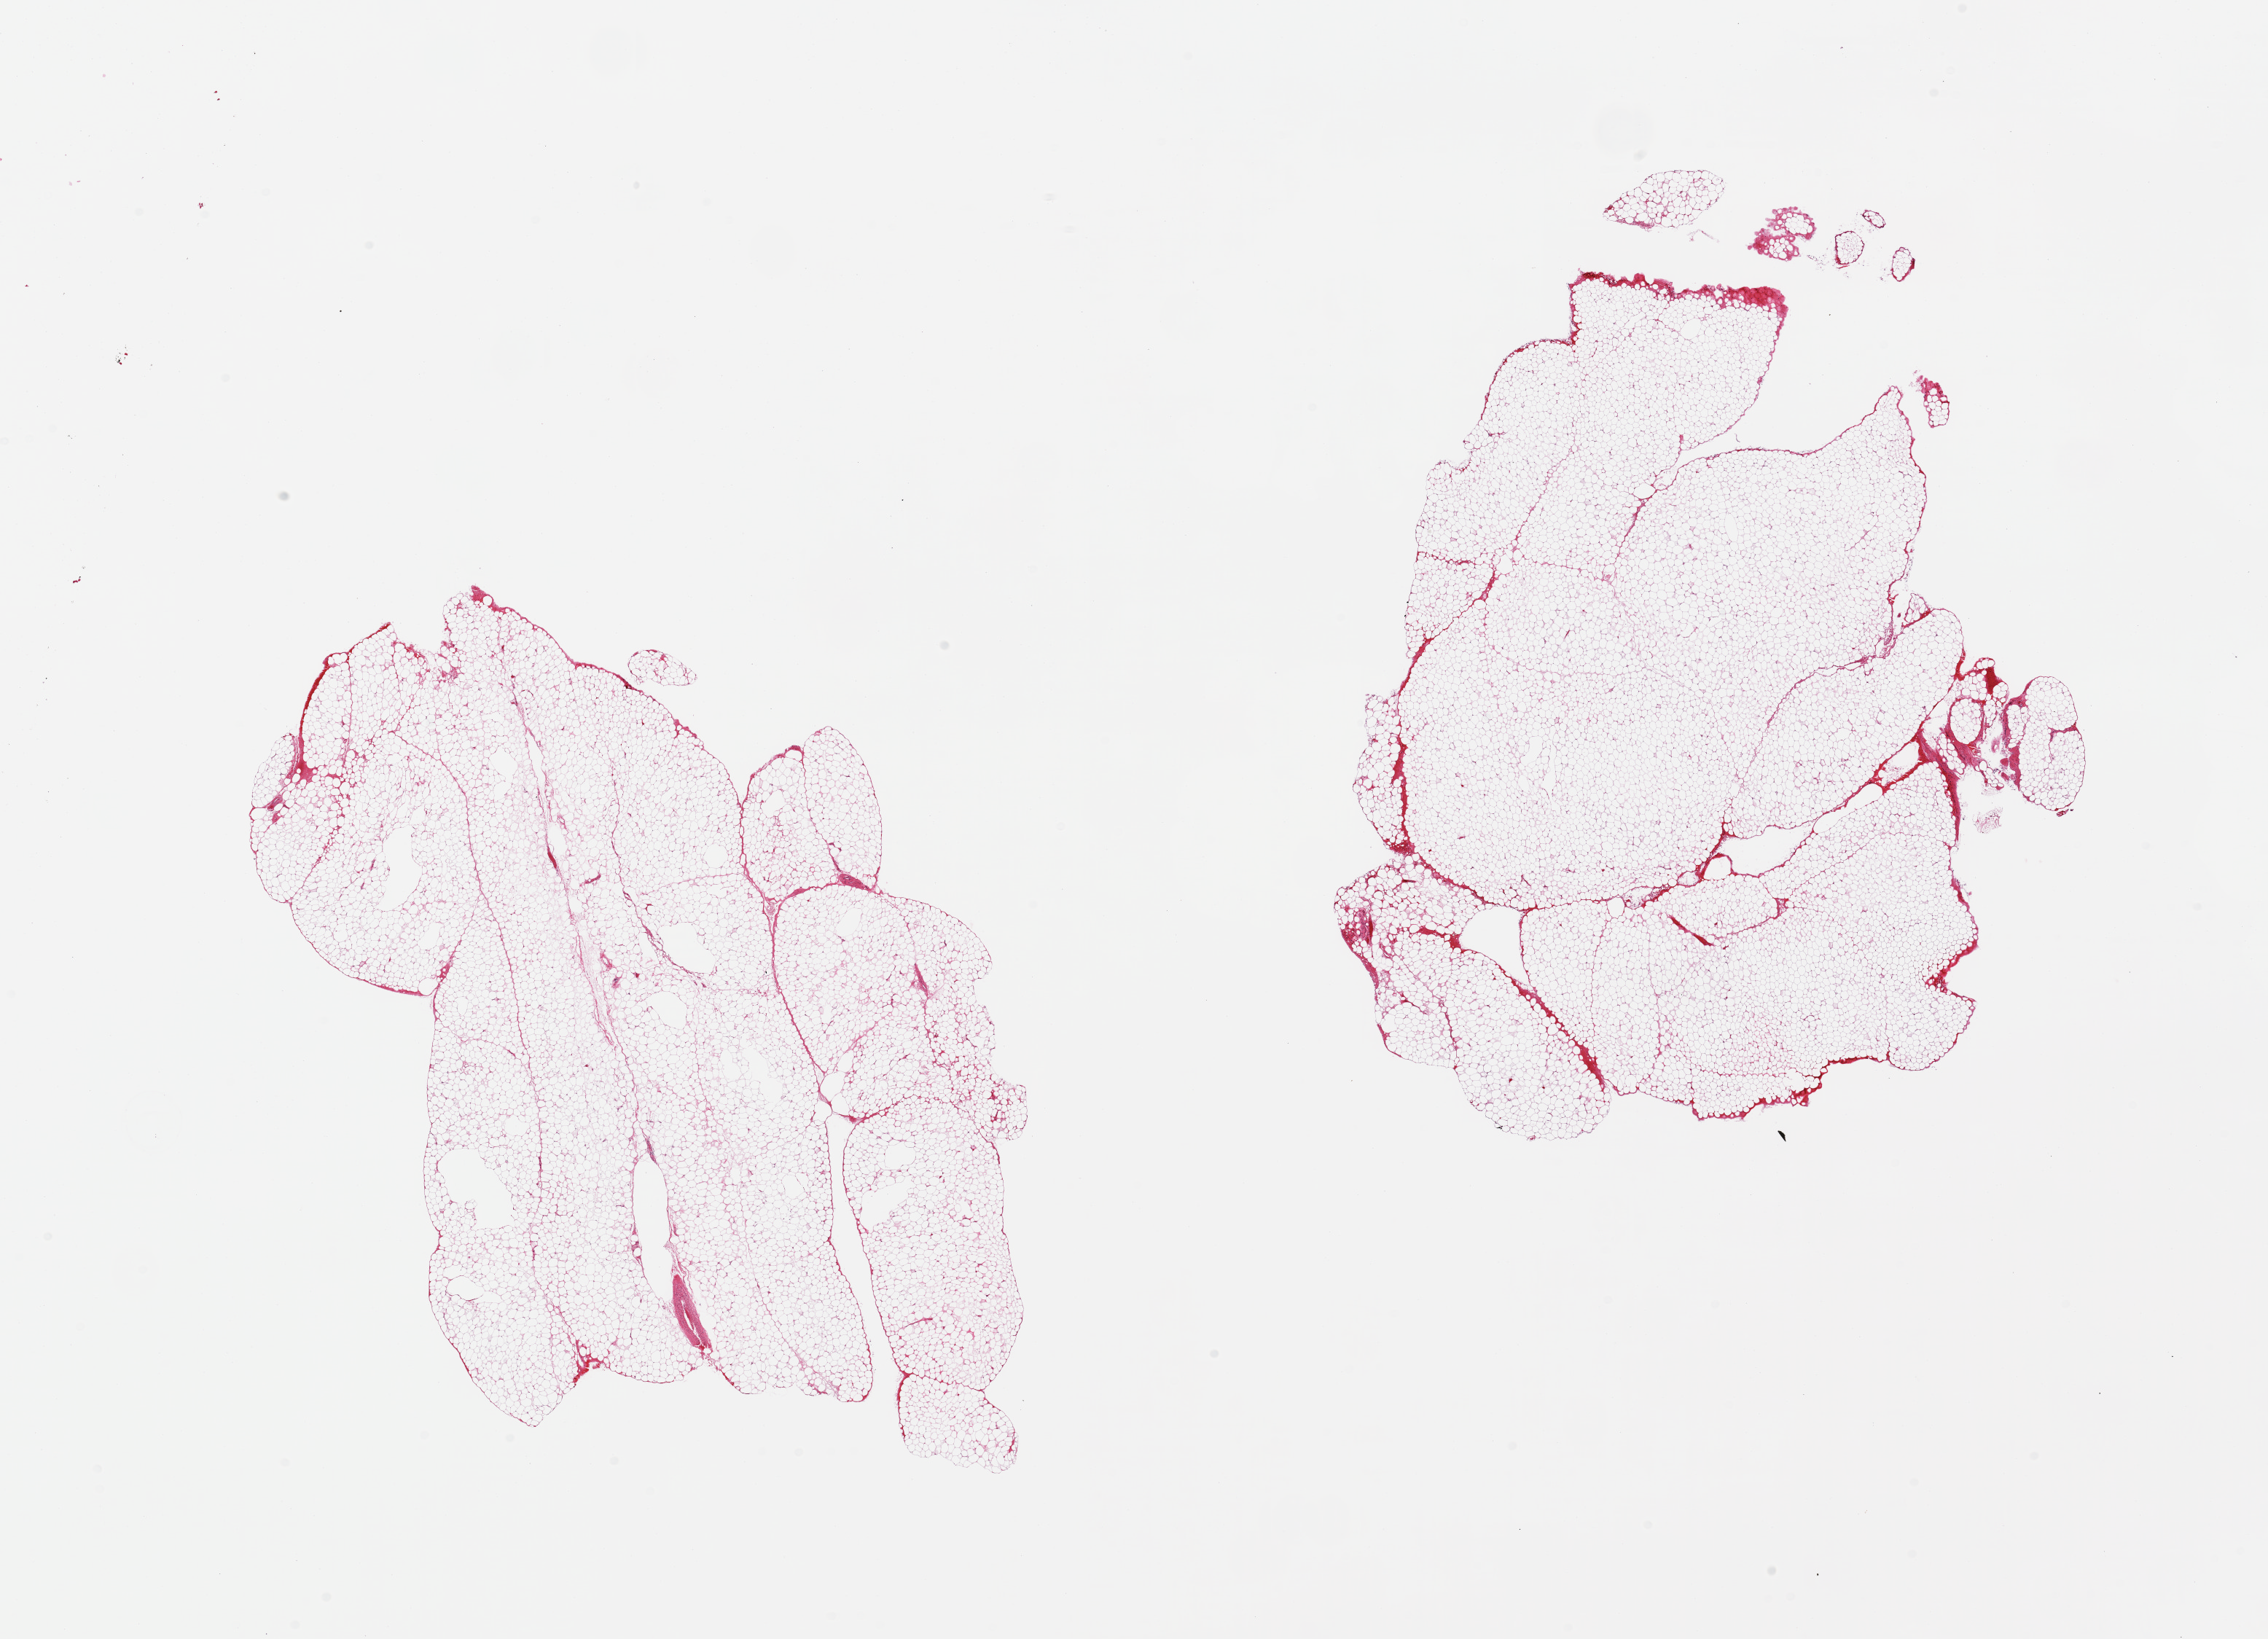
Haematoxylin and eosin whole-slide image, whole scanned area (about 24.6 x 17.8 mm) shown as a low-resolution overview, PAXgene-fixed paraffin-embedded (PFPE) section, target tissue: omentum, tissue donor sample.
Review note (as recorded): 2 pieces, trace mesothelial hyerplasia.